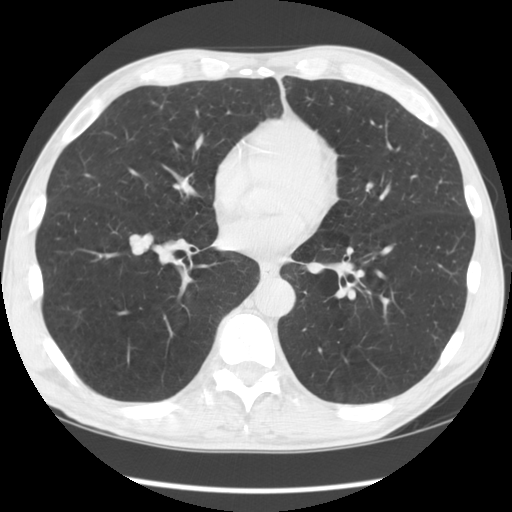
Chest CT (low-dose screening protocol), one axial image; second screening round (one year after baseline); lung window (W 1500 / L -600 HU); 2.5 mm slice thickness. Male, age 60 years at enrolment. Current smoker at enrolment.
Lesion marked by an expert reader, box from (x=112, y=227) to (x=161, y=268) px. The exam's reader record, not a measurement of the box and not confirmed to be the same lesion: non-calcified nodule or mass ≥4 mm, right lower lobe, 17 × 14 mm, smooth margins, soft tissue attenuation, pre-existing on the prior screen: yes; interval growth: yes. Official screen result: positive, other. Later outcome: lung cancer diagnosed 39 days after this screen — large cell carcinoma, NOS, right lower lobe, undifferentiated (G4), stage IA (AJCC 6th edition), 16 mm at pathology.